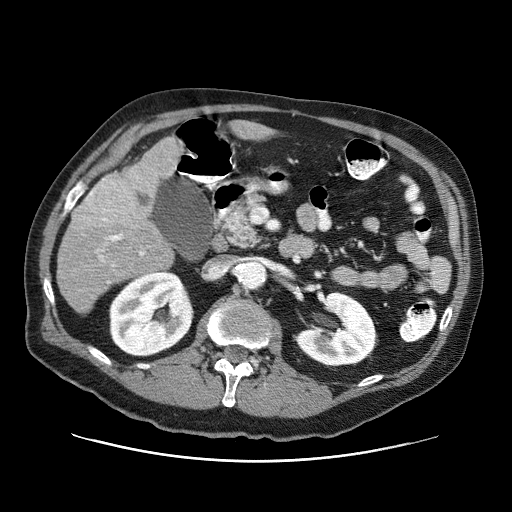
Contrast-enhanced abdominal CT (liver protocol), one axial slice; slice 27 of 87 in the series (ordered by position); reconstruction kernel STANDARD; 120 kVp; one of 3 acquisitions stored at this slice position; soft-tissue window (W 400 / L 40 HU); 512 × 512 image matrix, field of view 400 × 400 mm. Case-level facts recorded for this patient, not image findings: diagnosis: hepatocellular carcinoma (patient treated with transarterial chemoembolisation; whether this scan precedes or follows treatment is not stated here); TNM stage (as recorded): Stage-IIIA; Child-Pugh class: A; tumour differentiation: well differentiated; tumour nodularity: multinodular.
Outlined on this slice (semi-automatic segmentation, software-assisted and operator-edited):
- liver parenchyma outside the tumour (the mass and vessels are separate outlines, so this box may not span the whole liver): box from (x=56, y=136) to (x=182, y=314) px
- mass: (x=72, y=162)–(x=157, y=226)
- liver vessels: (x=100, y=218)–(x=144, y=266)